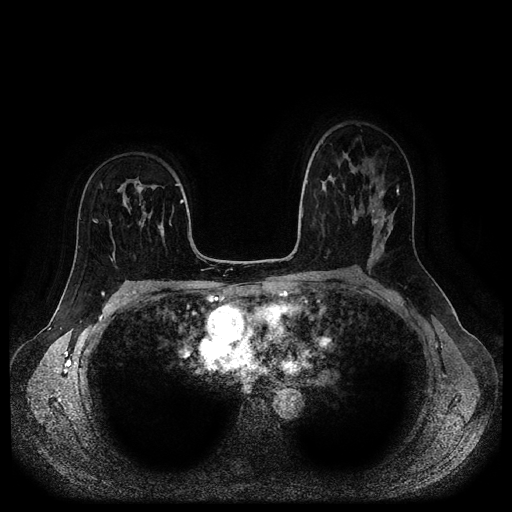
Breast MRI (dynamic contrast-enhanced, multi-phase), one axial slice. Slice 62 of 116 in the series (ordered by position). Dynamic contrast-enhanced series, time point 2 of 5 at this slice position (early post-contrast). 1.5 T. TE 2.6 ms, TR 5.3 ms. 512 × 512 image matrix. Female patient, age 50 years.
Annotated regions visible in this slice (semi-automatically segmented with operator editing):
- breast lesion (labelled benign in the annotation): bounding box <120,192,133,215> (left, top, right, bottom; pixels)